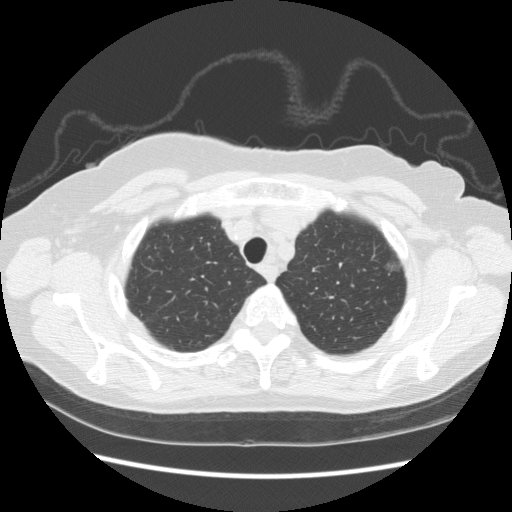
Axial slice from a low-dose chest CT screening exam, first (baseline) screen, lung window (W 1500 / L -600 HU), 2.5 mm slice thickness, standard (soft-tissue) reconstruction kernel (STANDARD), slice 30 of 247 in the series. Female participant, aged 73 years at enrolment. Former smoker at enrolment.
- Lesion marked by an expert reader, box from (x=371, y=233) to (x=412, y=281) px.
- The screening reader recorded 3 non-calcified nodules or masses ≥4 mm on this exam (left upper lobe, left upper lobe, left upper lobe); which of them this box marks is not recorded.
- Official screen result: positive, change unspecified: nodule(s) >= 4 mm or enlarging nodule(s), mass(es), or other non-specific abnormalities suspicious for lung cancer.
- Later outcome: lung cancer diagnosed 445 days after this screen — bronchiolo-alveolar adenocarcinoma, NOS, left upper lobe, well differentiated (G1), stage IA (AJCC 6th edition), 10 mm at pathology.